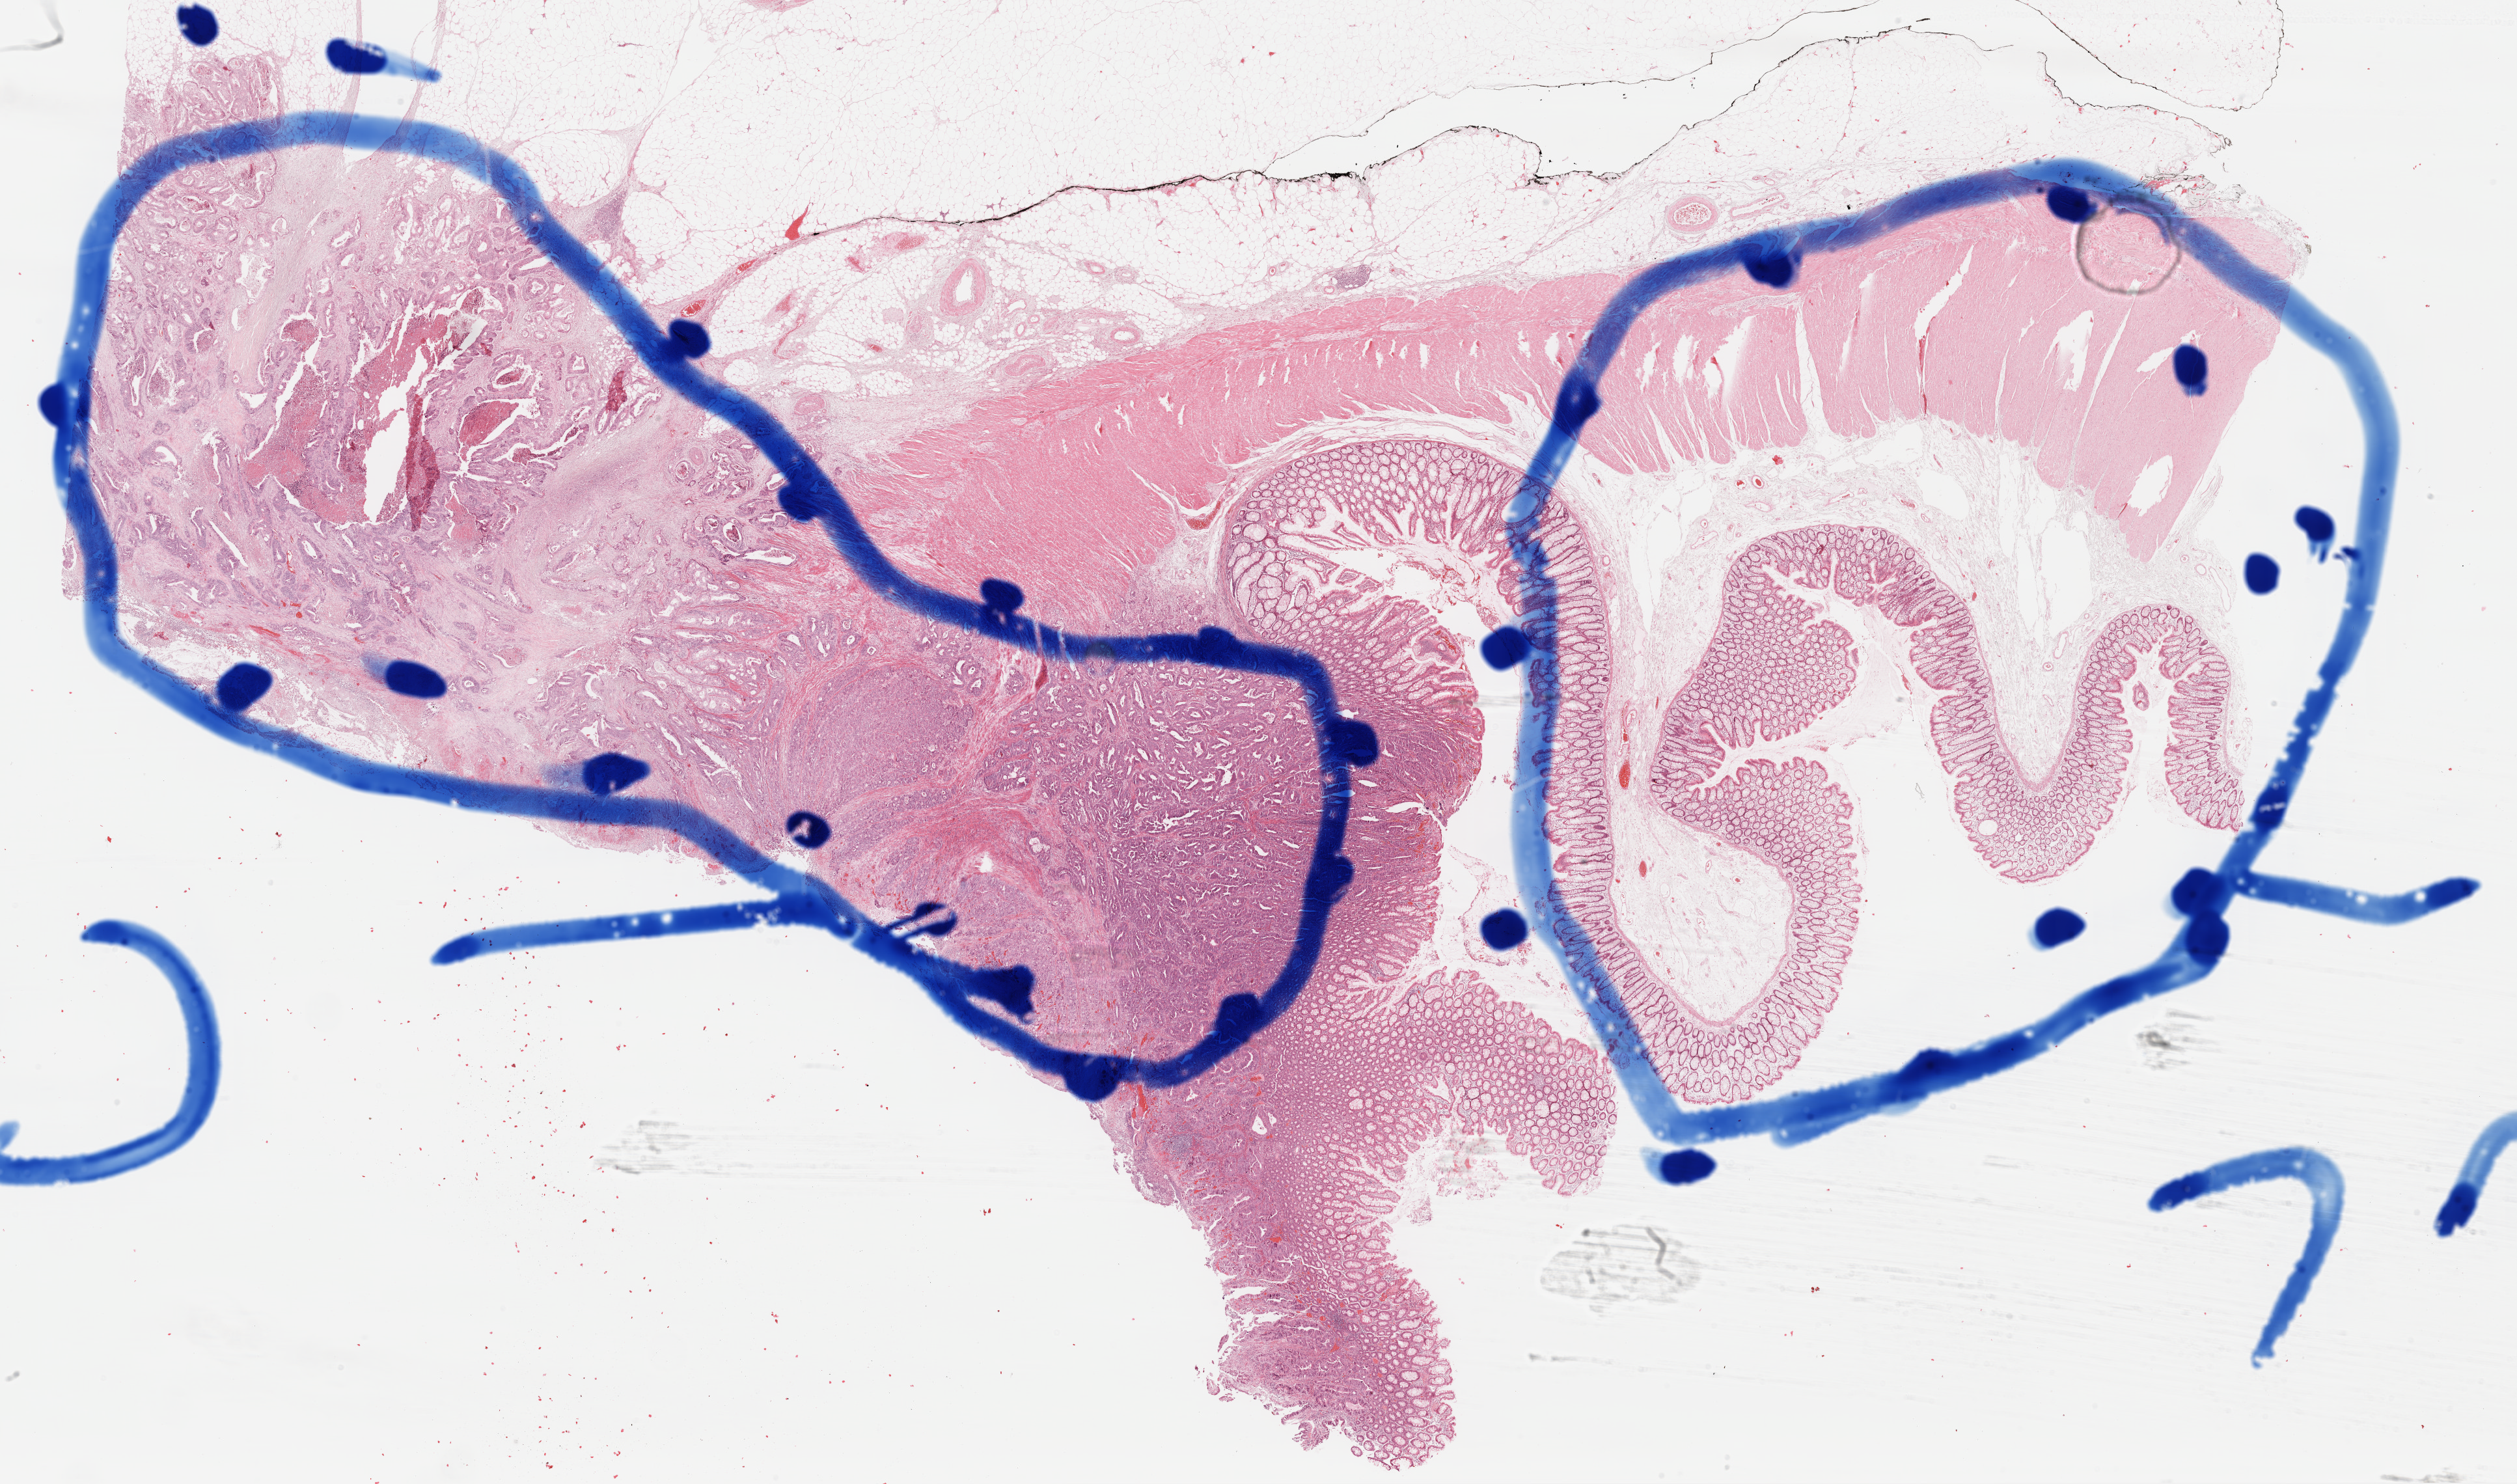
Digitized H&E tissue section (whole slide), low-resolution overview of the scanned area, about 30.5 x 18.0 mm, formalin-fixed paraffin-embedded (FFPE) diagnostic section, colon, primary tumour sample. Patient: female, age at initial diagnosis 79 years.
Pathologic diagnosis: Adenocarcinoma, NOS (sigmoid colon). Lymph nodes positive (case pathology): 2 of 10 examined. AJCC pathologic stage: IIA.